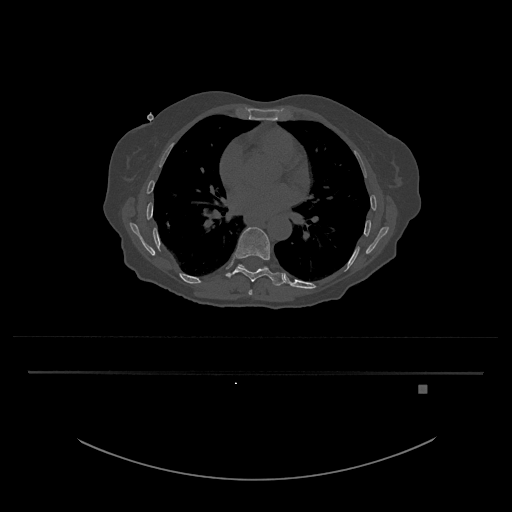
CT including the spine, one axial slice; reconstruction kernel Br40s/3; 120 kVp; bone window (W 1800 / L 400 HU); 0.5 mm slice thickness; 512 × 512 image matrix, field of view 500 × 500 mm. Female patient, age 57 years. Case-level facts recorded for this patient, not image findings: primary cancer: cervical.
Annotated regions visible in this slice (semi-automatic segmentation, software-assisted and operator-edited):
- T10 vertebra: bounding box (x1, y1, x2, y2) in pixels: (238, 264, 268, 272)
- T8 vertebra: (248, 289, 253, 295)
- T9 vertebra: (226, 227, 284, 286)